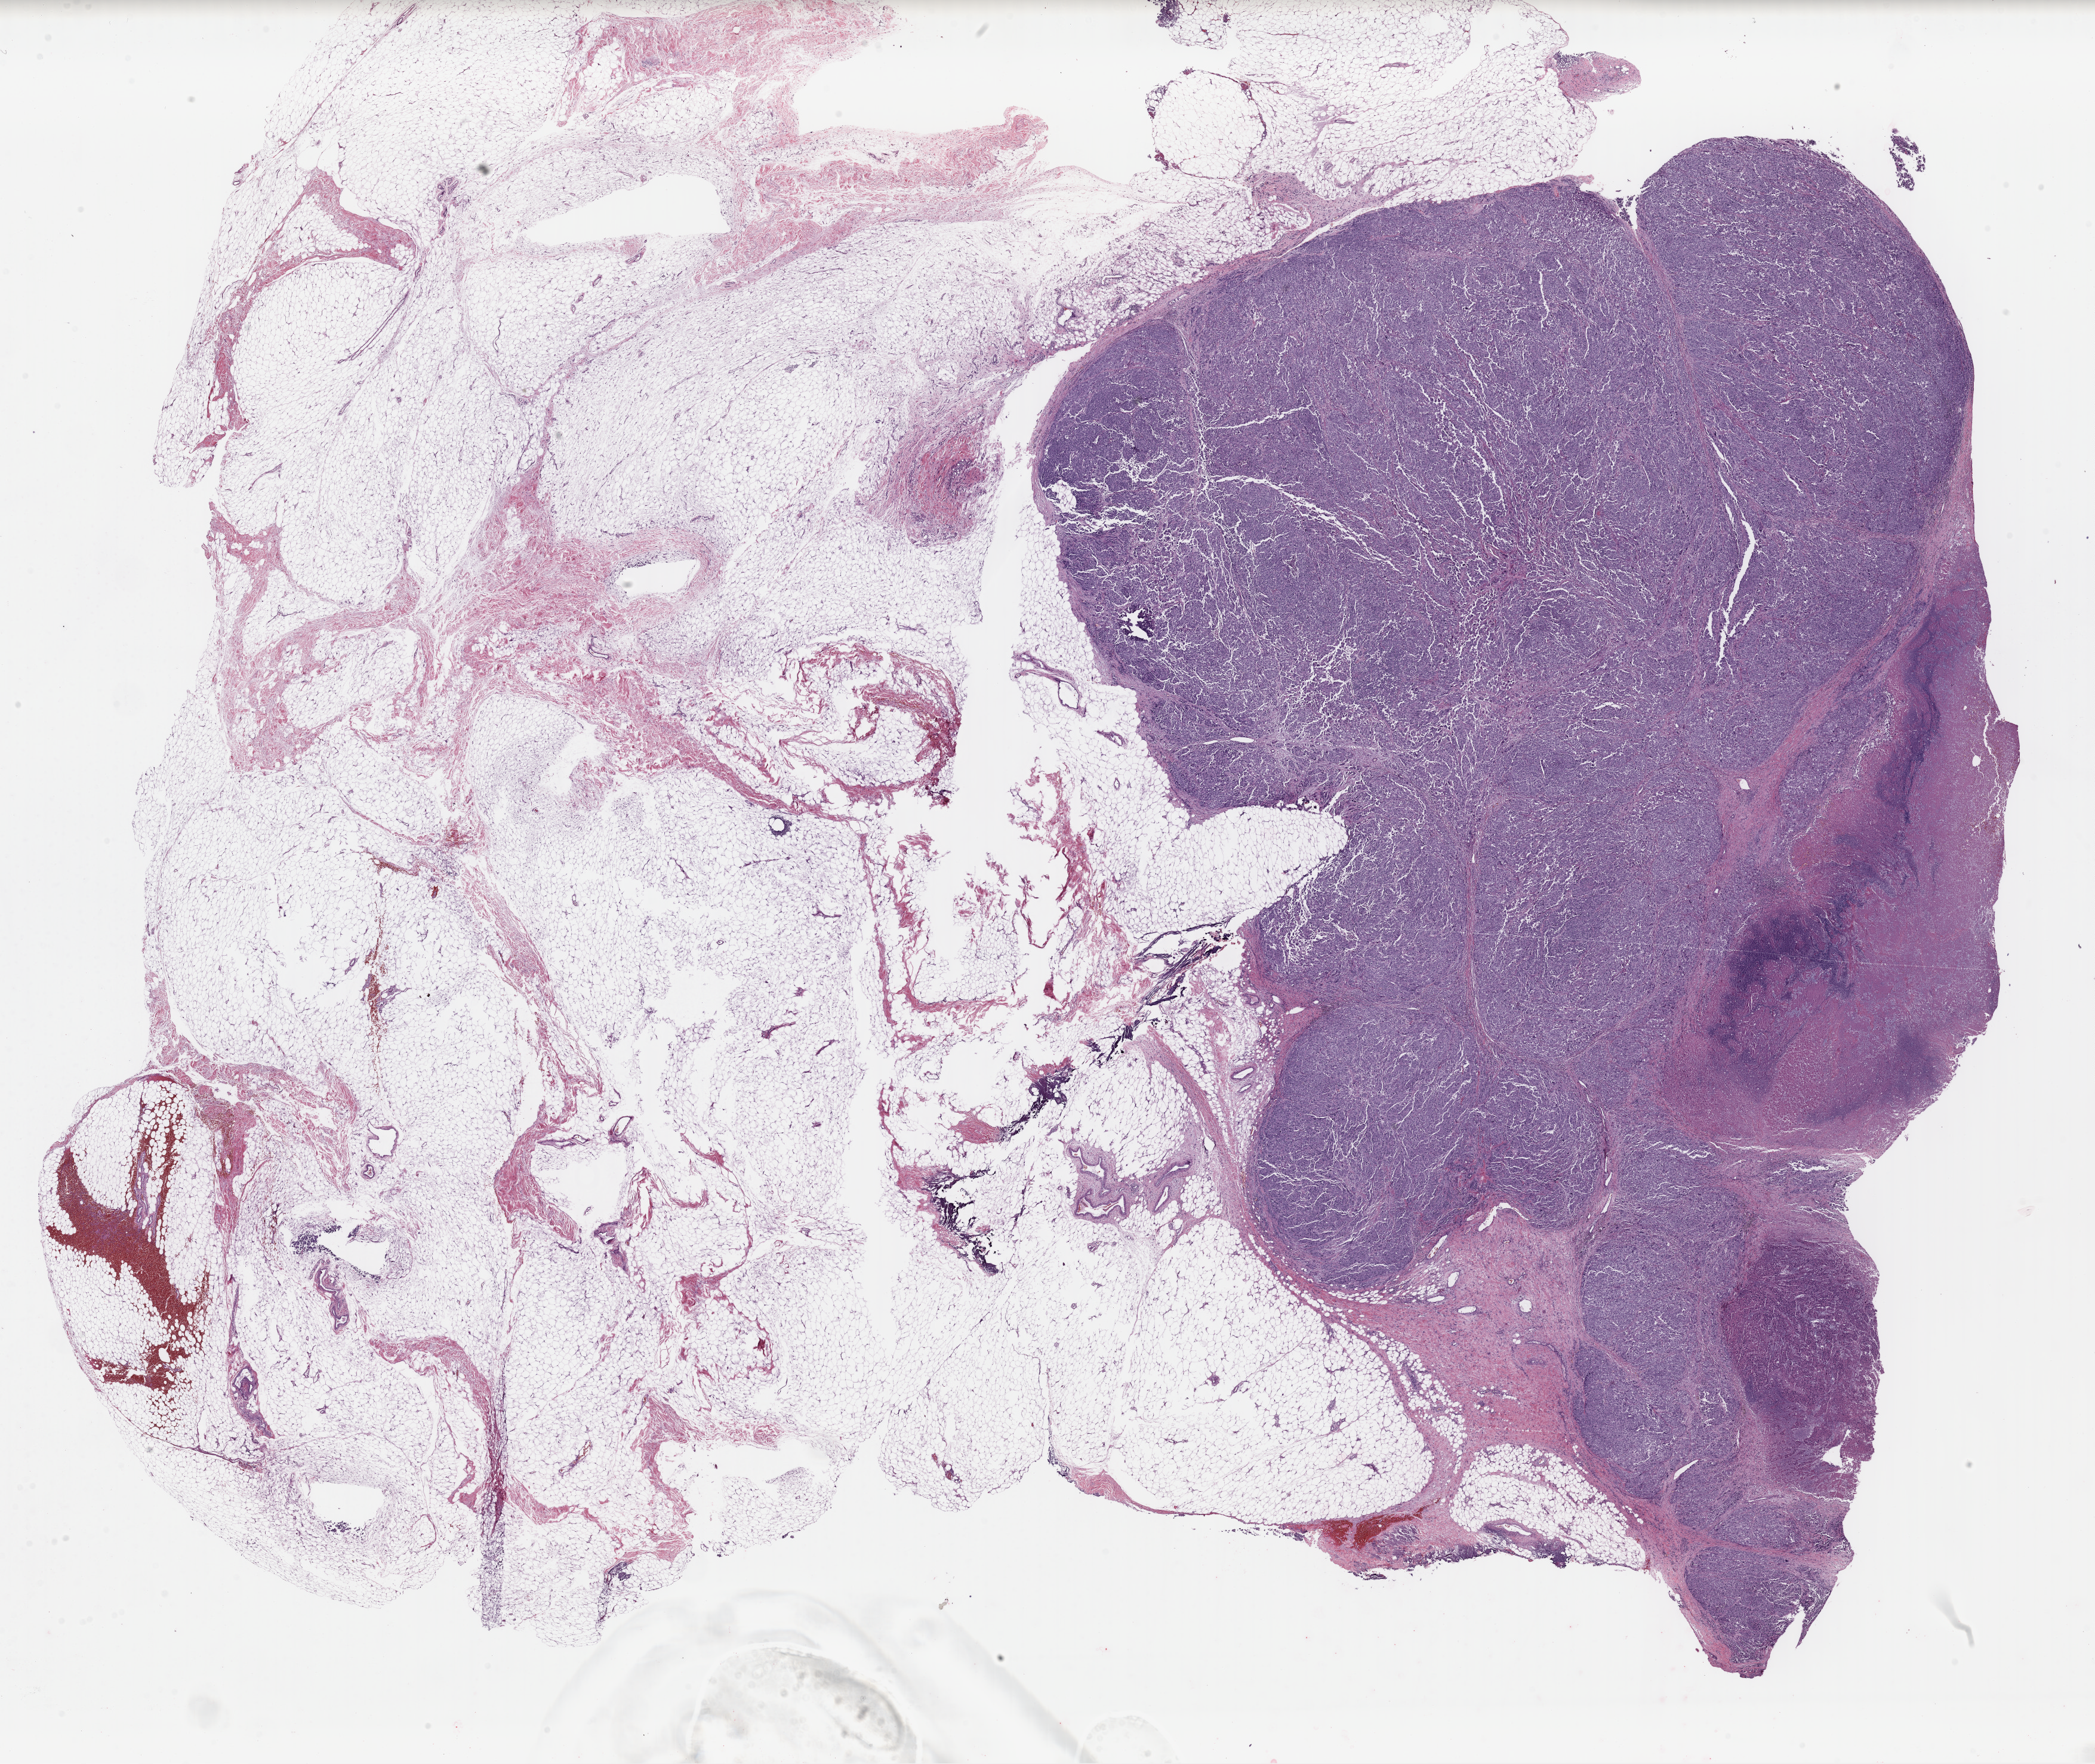
H&E-stained whole-slide image — whole scanned area (about 27.7 x 23.3 mm, from a 40x scan) shown as a low-resolution overview, FFPE section, primary tumour sample from the skin. Female patient; age at initial diagnosis 57 years.
Diagnosis: Malignant melanoma, NOS.